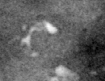
Crop from a digitized film mammogram around one marked abnormality, right breast, CC view.
Calcifications, morphology pleomorphic, distribution clustered; BI-RADS assessment category 4; pathology result (as recorded, not read from the image): malignant.